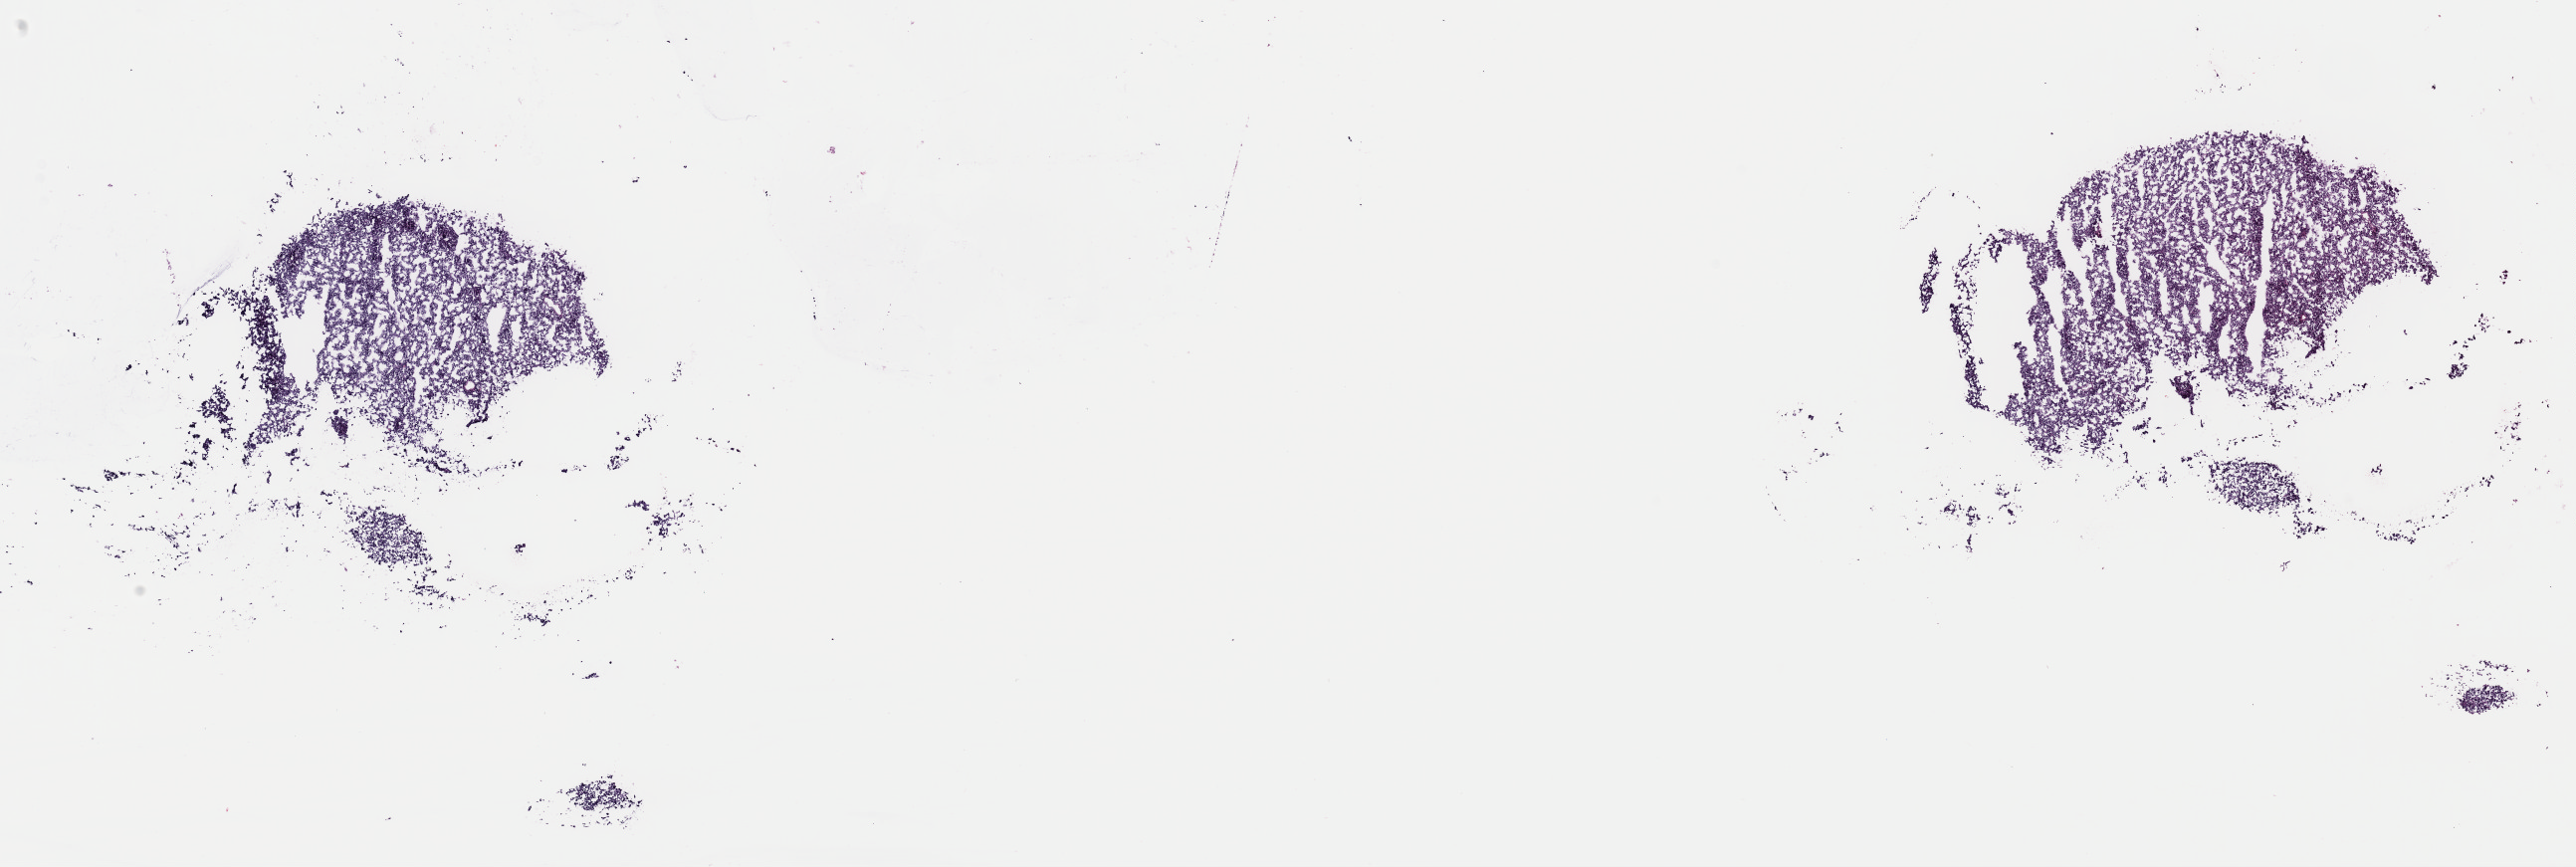
Digitized H&E-stained tissue section (whole slide), shown as a low-resolution overview of the whole scanned area (about 20.4 x 6.9 mm); frozen section from the top of the tissue portion; primary tumour sample from the adrenal gland. Female, age 66 years at initial diagnosis. Composition of this section per pathologist review: tumour cells 100%, tumour nuclei 80%, normal cells 0%, stromal cells 0%, necrosis 0%. Infiltration values recorded for this section: lymphocyte infiltration 1%, monocyte infiltration 0%, neutrophil infiltration 0%.
• pathologic diagnosis: Pheochromocytoma, NOS
• laterality: right